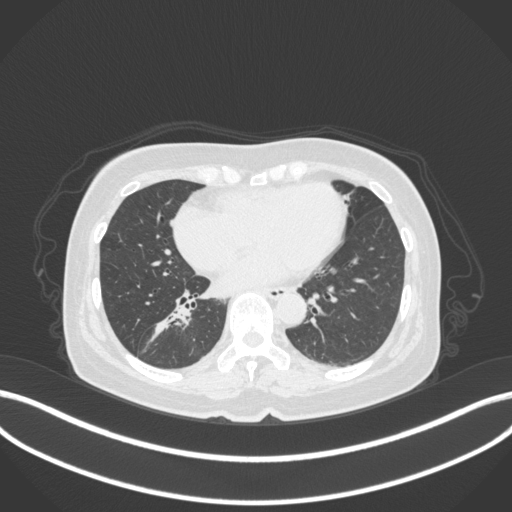
Chest CT, one axial slice. Reconstruction kernel B31f. Lung window (W 1500 / L -600 HU). 512 × 512 image matrix, field of view 400 × 400 mm. Female patient, age 67 years. From the clinical record (not read from this slice): clinical TNM (as recorded): T1c N1 M0; histopathological grade: G2-3.
Annotated regions visible in this slice (bounding box drawn by a radiologist):
- lung tumour (recorded histology: adenocarcinoma): bounding box <148,310,195,340> (left, top, right, bottom; pixels)